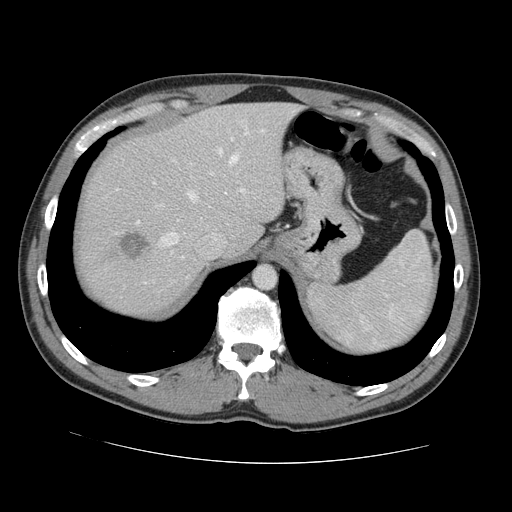
Contrast-enhanced abdominal CT, one axial slice. 120 kVp. Intravenous contrast given. Soft-tissue window (W 400 / L 40 HU). 2.5 mm slice thickness. 512 × 512 image matrix, field of view 380 × 380 mm. Male patient, age 40 years. From the clinical record (not read from this slice): diagnosis: colorectal cancer liver metastases, imaged before liver resection; multiple liver metastases: yes.
Annotated regions visible in this slice (manually delineated by an expert):
- hepatic veins: bounding box <161,149,238,246> (left, top, right, bottom; pixels)
- liver: <75,104,295,316>
- planned liver remnant (the part of the liver to remain after resection): <103,104,297,255>
- portal vein (with intrahepatic branches): <211,132,249,193>
- liver metastasis: <119,230,148,262>